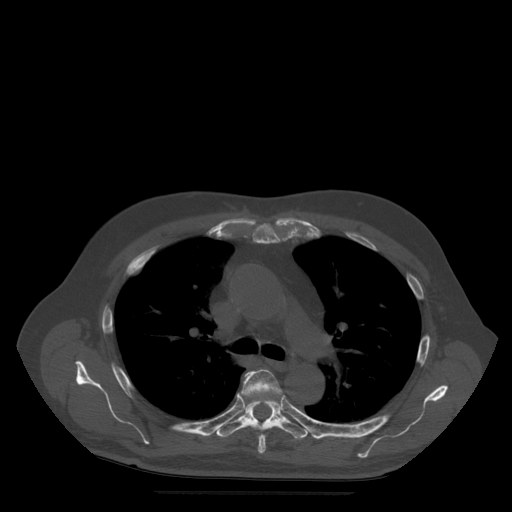
CT including the spine, one axial slice; slice 362 of 522 in the series (ordered by position); bone window (W 1800 / L 400 HU); 1.25 mm slice thickness; 512 × 512 image matrix, field of view 420 × 420 mm. Patient age 72 years. Case-level facts recorded for this patient, not image findings: primary cancer: prostate.
Structures marked on this image (semi-automatically segmented with operator editing):
- T5 vertebra: bounding box <241,369,283,454> (left, top, right, bottom; pixels)
- T6 vertebra: <217,376,309,440>